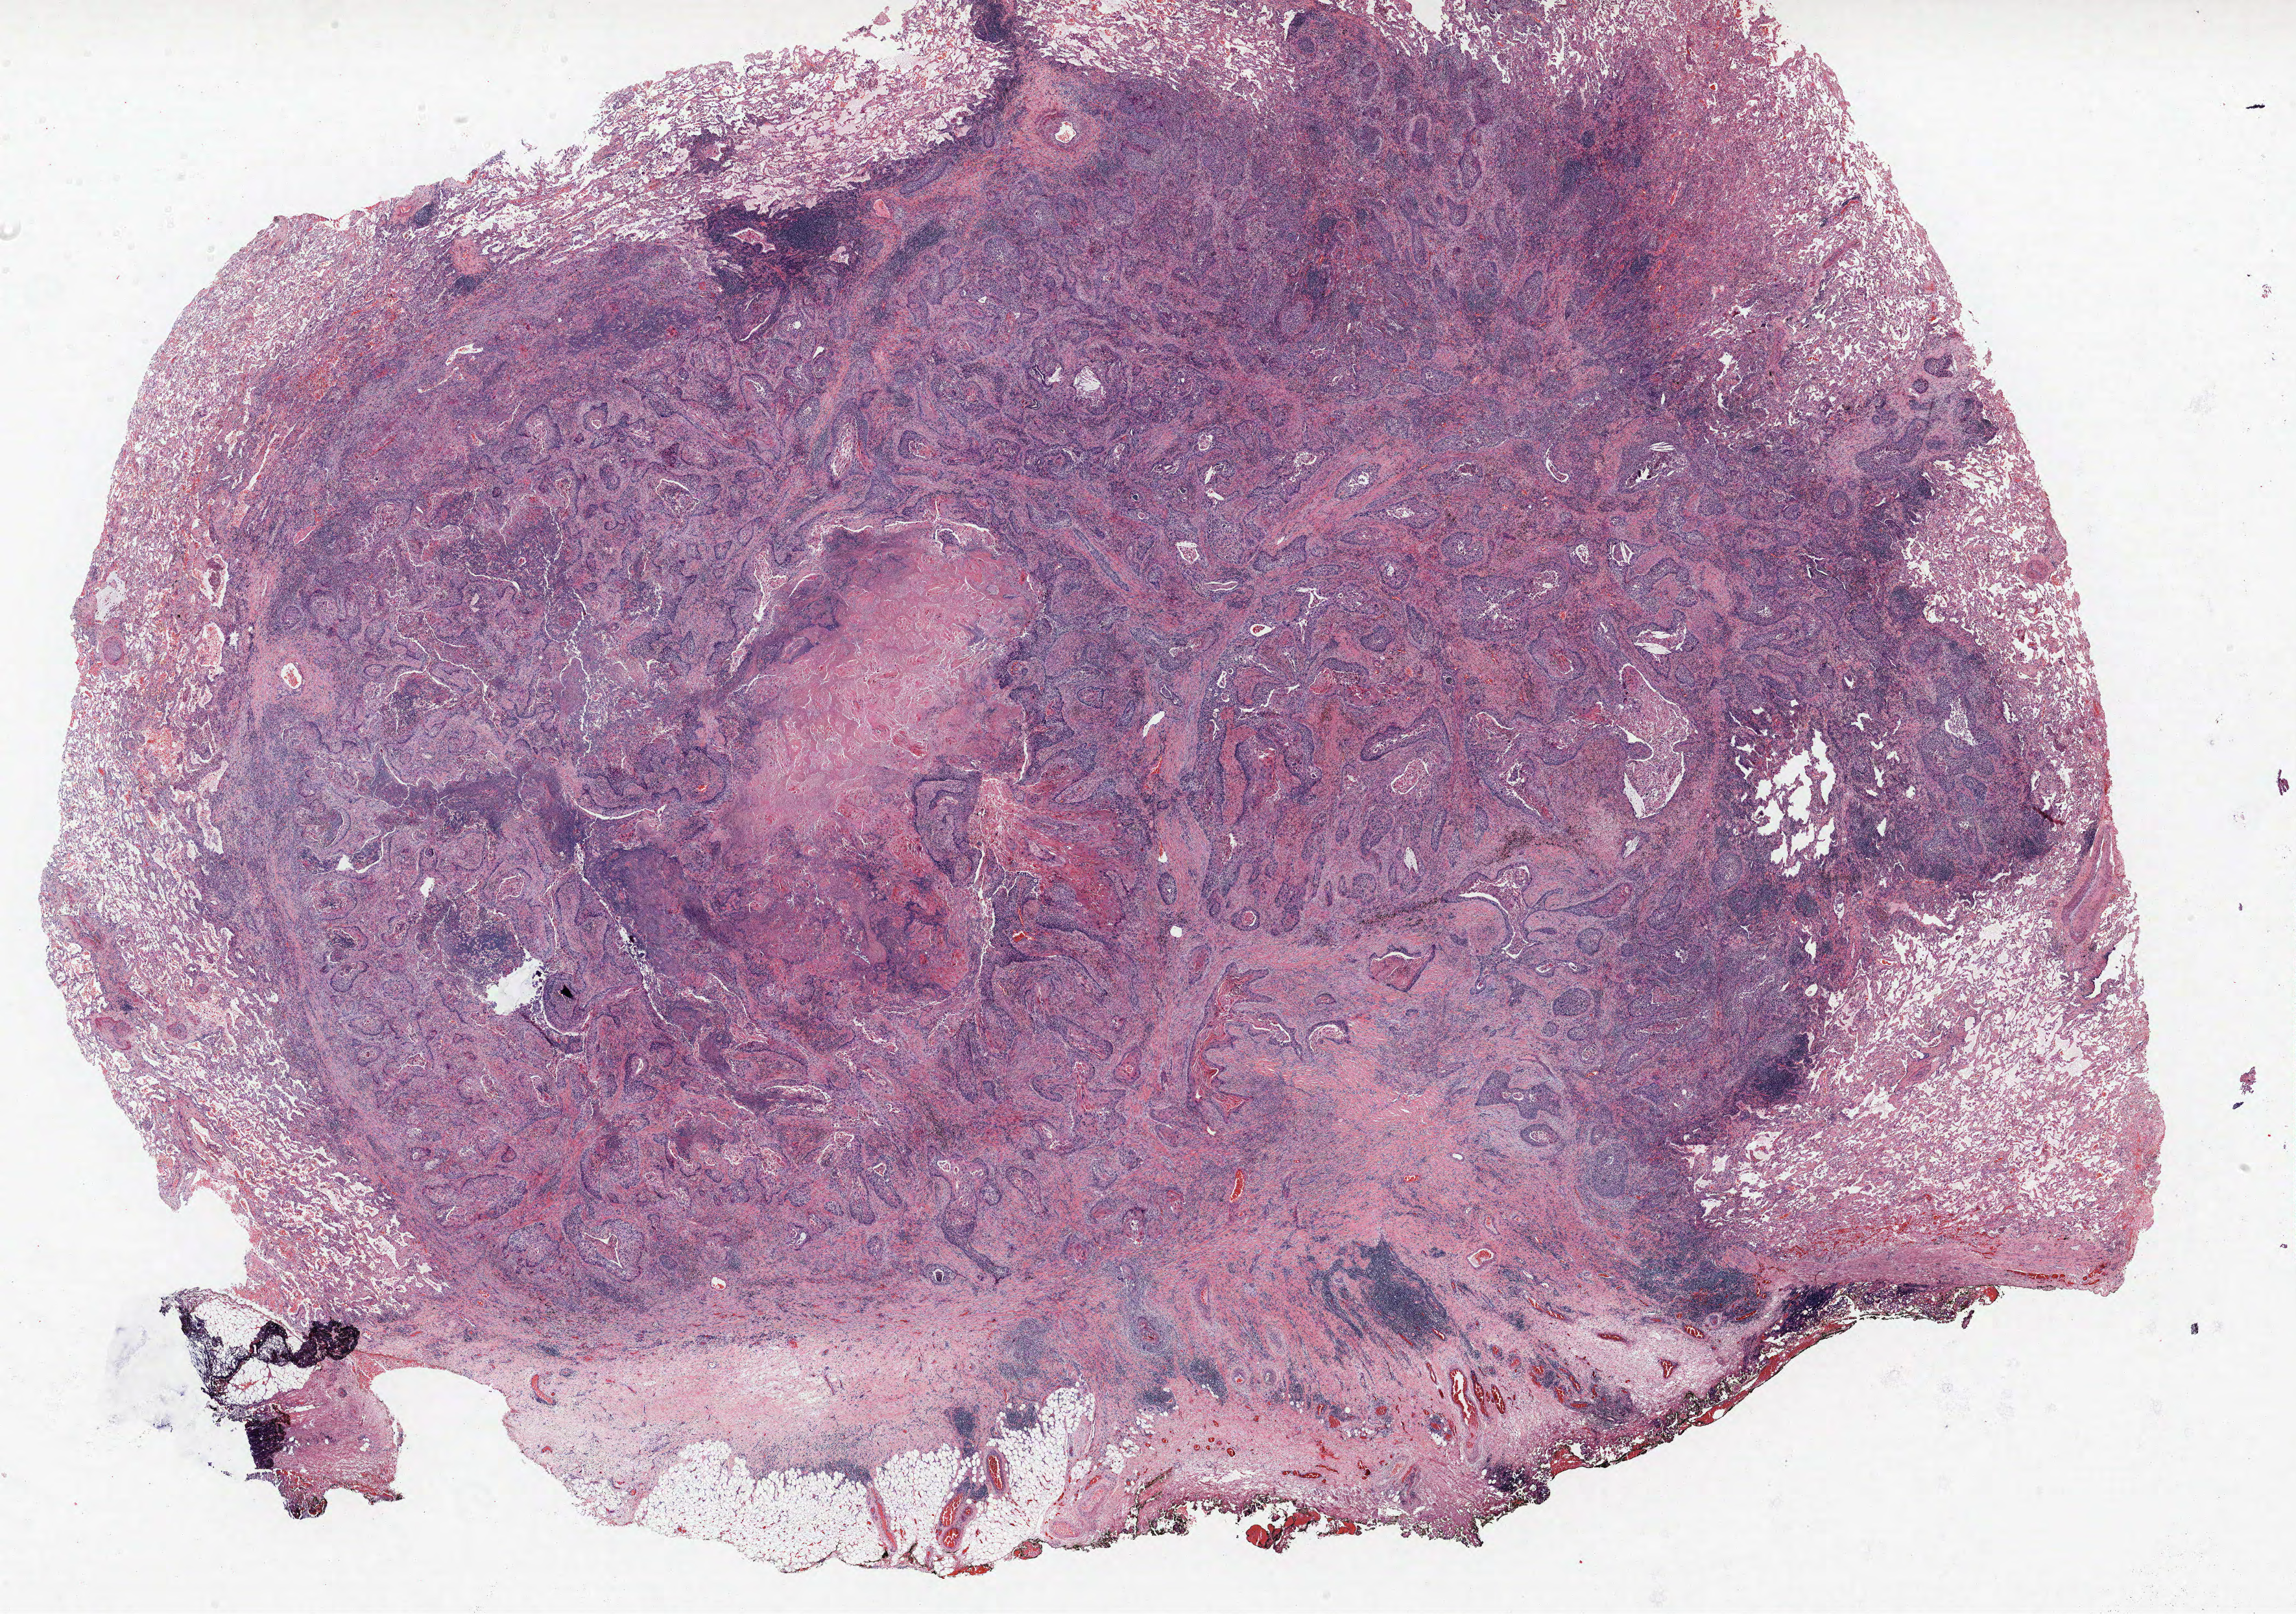
Whole-slide histology image, Hematoxylin and eosin (H&E) stained — low-resolution overview of the scanned area, about 28.3 x 19.9 mm (slide scanned at 40x), formalin-fixed paraffin-embedded (FFPE) section, lung tissue. Female patient, aged 59 at enrolment. Current smoker at enrolment. Grade: moderately differentiated (G2).
Stage (AJCC 6th edition): IB. Participant's lung-cancer diagnosis: Squamous cell carcinoma, NOS. Tumour size (pathology): 28 mm. Primary tumour location (clinical record): right upper lobe.